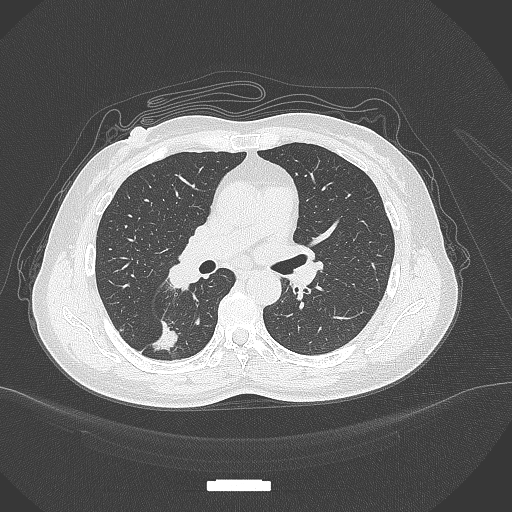
Chest CT, one axial slice; slice 172 of 352 in the series (ordered by position); 120 kVp; lung window (W 1500 / L -600 HU); 1 mm slice thickness; 512 × 512 image matrix, field of view 400 × 400 mm. Patient: female, 55 years. From the clinical record (not read from this slice): clinical TNM (as recorded): T1c N1 M0.
Outlined on this slice (bounding box drawn by a radiologist):
- lung tumour (recorded histology: adenocarcinoma): bounding box <148,315,181,355> (left, top, right, bottom; pixels)